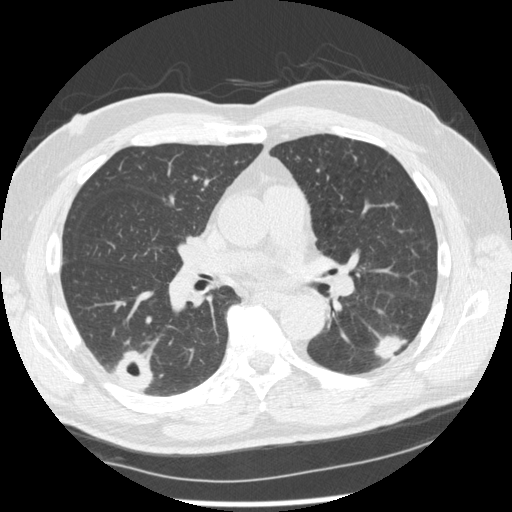
Low-dose screening chest CT, axial slice. Second annual screen. Lung window (W 1500 / L -600 HU). 1.25 mm slice thickness. 512 × 512 image matrix, field of view 360 × 360 mm. Male participant, aged 74 years at enrolment. Former smoker at enrolment.
Expert-annotated lung lesion, box from (x=369, y=315) to (x=422, y=369) px. The screening reader recorded 7 non-calcified nodules or masses ≥4 mm on this exam; which of them this box marks is not recorded. Participant outcome: lung cancer diagnosed 43 days after this screen — squamous cell carcinoma, NOS, left lower lobe, well differentiated (G1), stage IA (AJCC 6th edition), 28 mm at pathology.